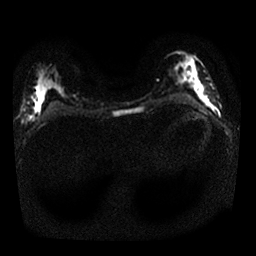
Breast MRI, one axial slice; position 11 of 25 along the scan axis; diffusion-weighted series; image 2 of 4 stored at this slice position (different b-values; order by instance number); 1.5 T; 4 mm slice thickness; 256 × 256 image matrix, field of view 320 × 320 mm. Female patient.
Annotated regions visible in this slice (manually delineated by an expert):
- tumour on diffusion-weighted imaging: bounding box [x1, y1, x2, y2] px = [202, 96, 206, 101]